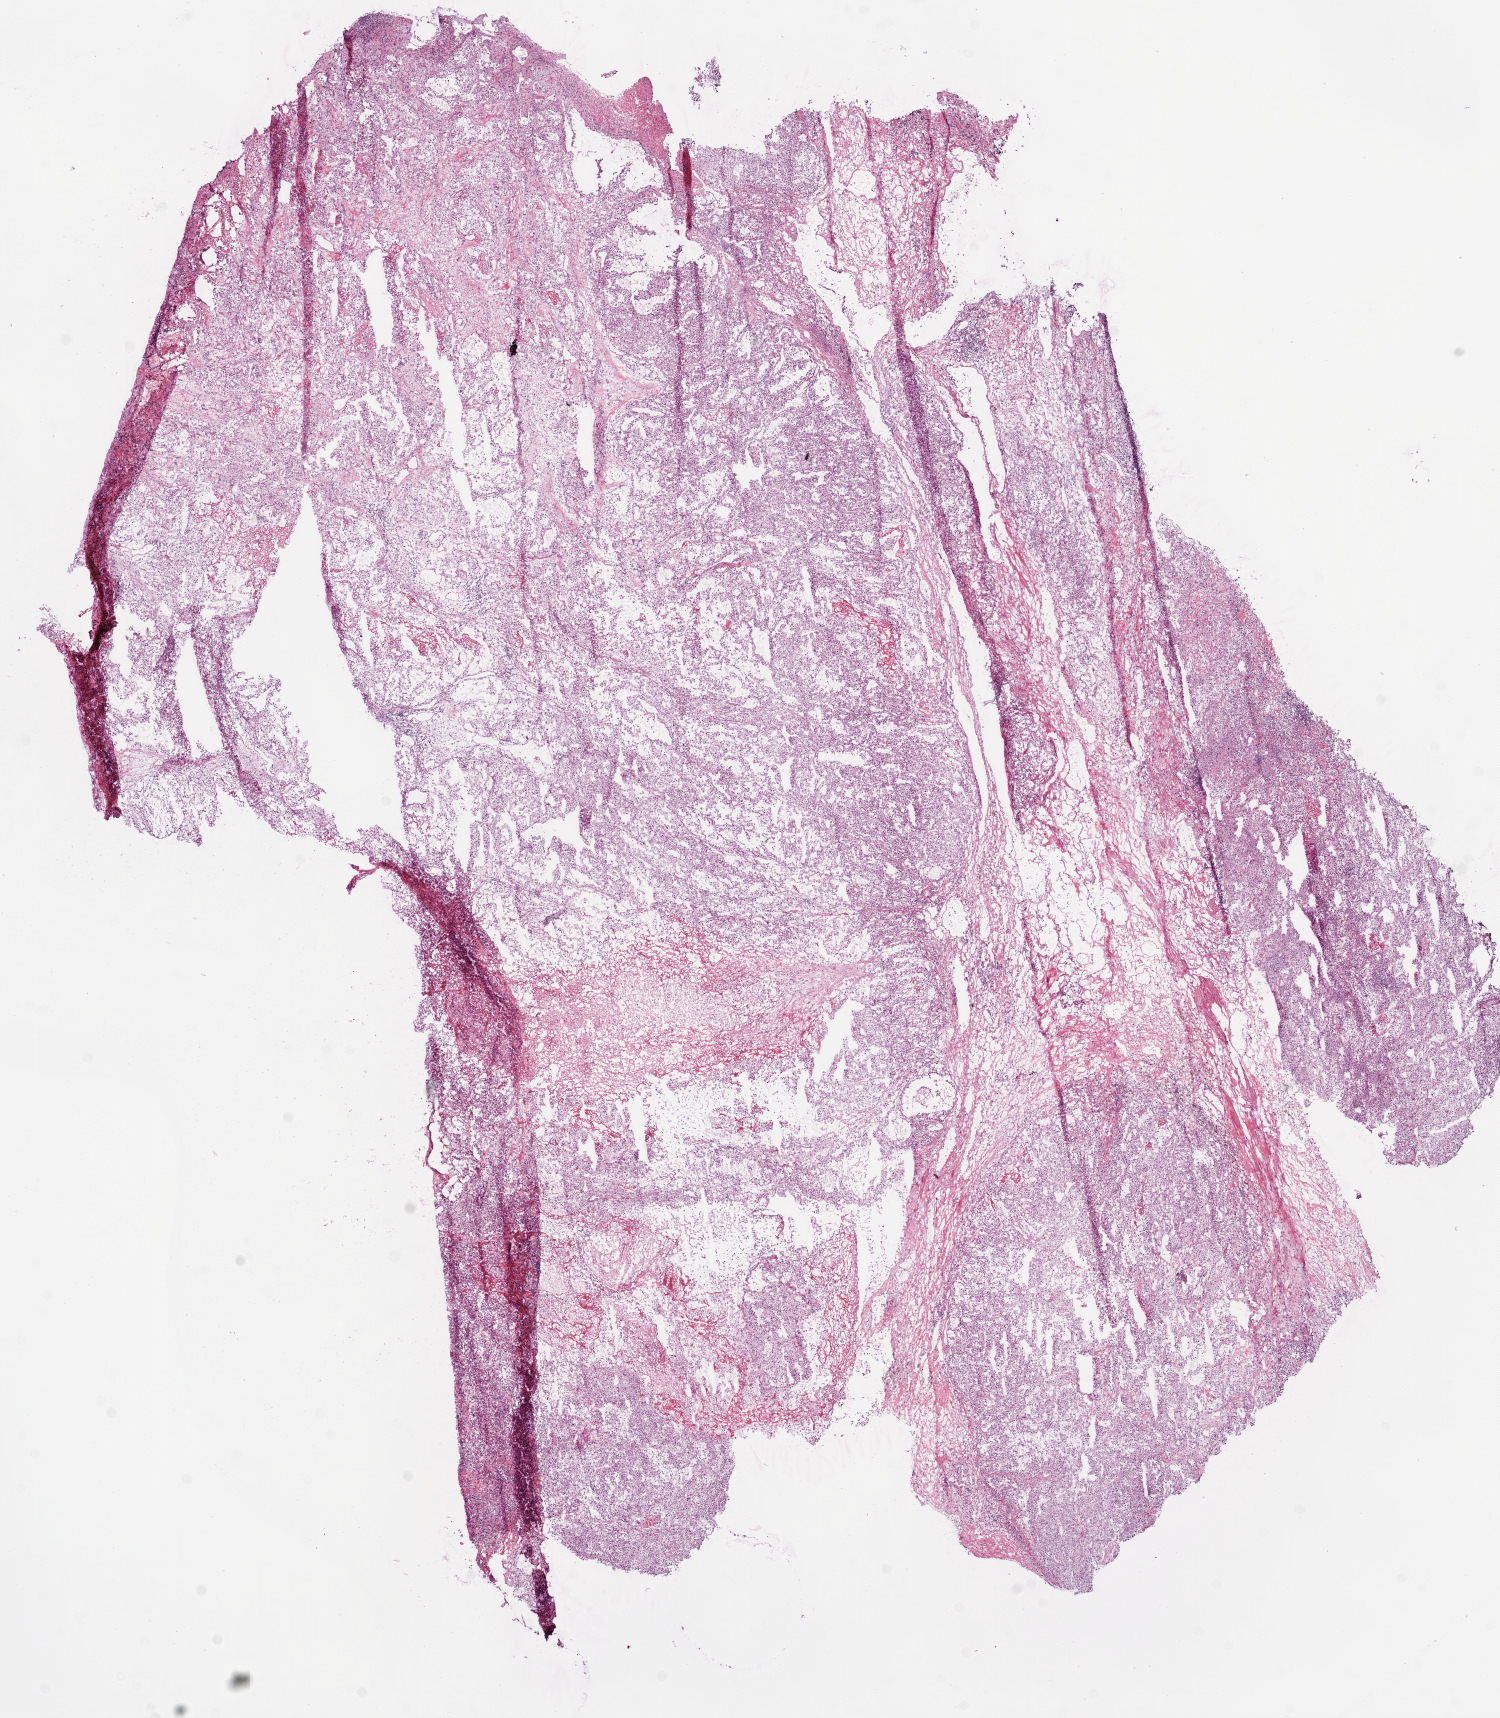
Digitized H&E-stained tissue section (whole slide), a low-resolution overview of the entire scanned area, about 12.0 x 13.8 mm. Frozen section from the bottom of the tissue portion. Kidney, primary tumour sample. Male, age 58 years at initial diagnosis.
Pathologic diagnosis: Clear cell adenocarcinoma, NOS.